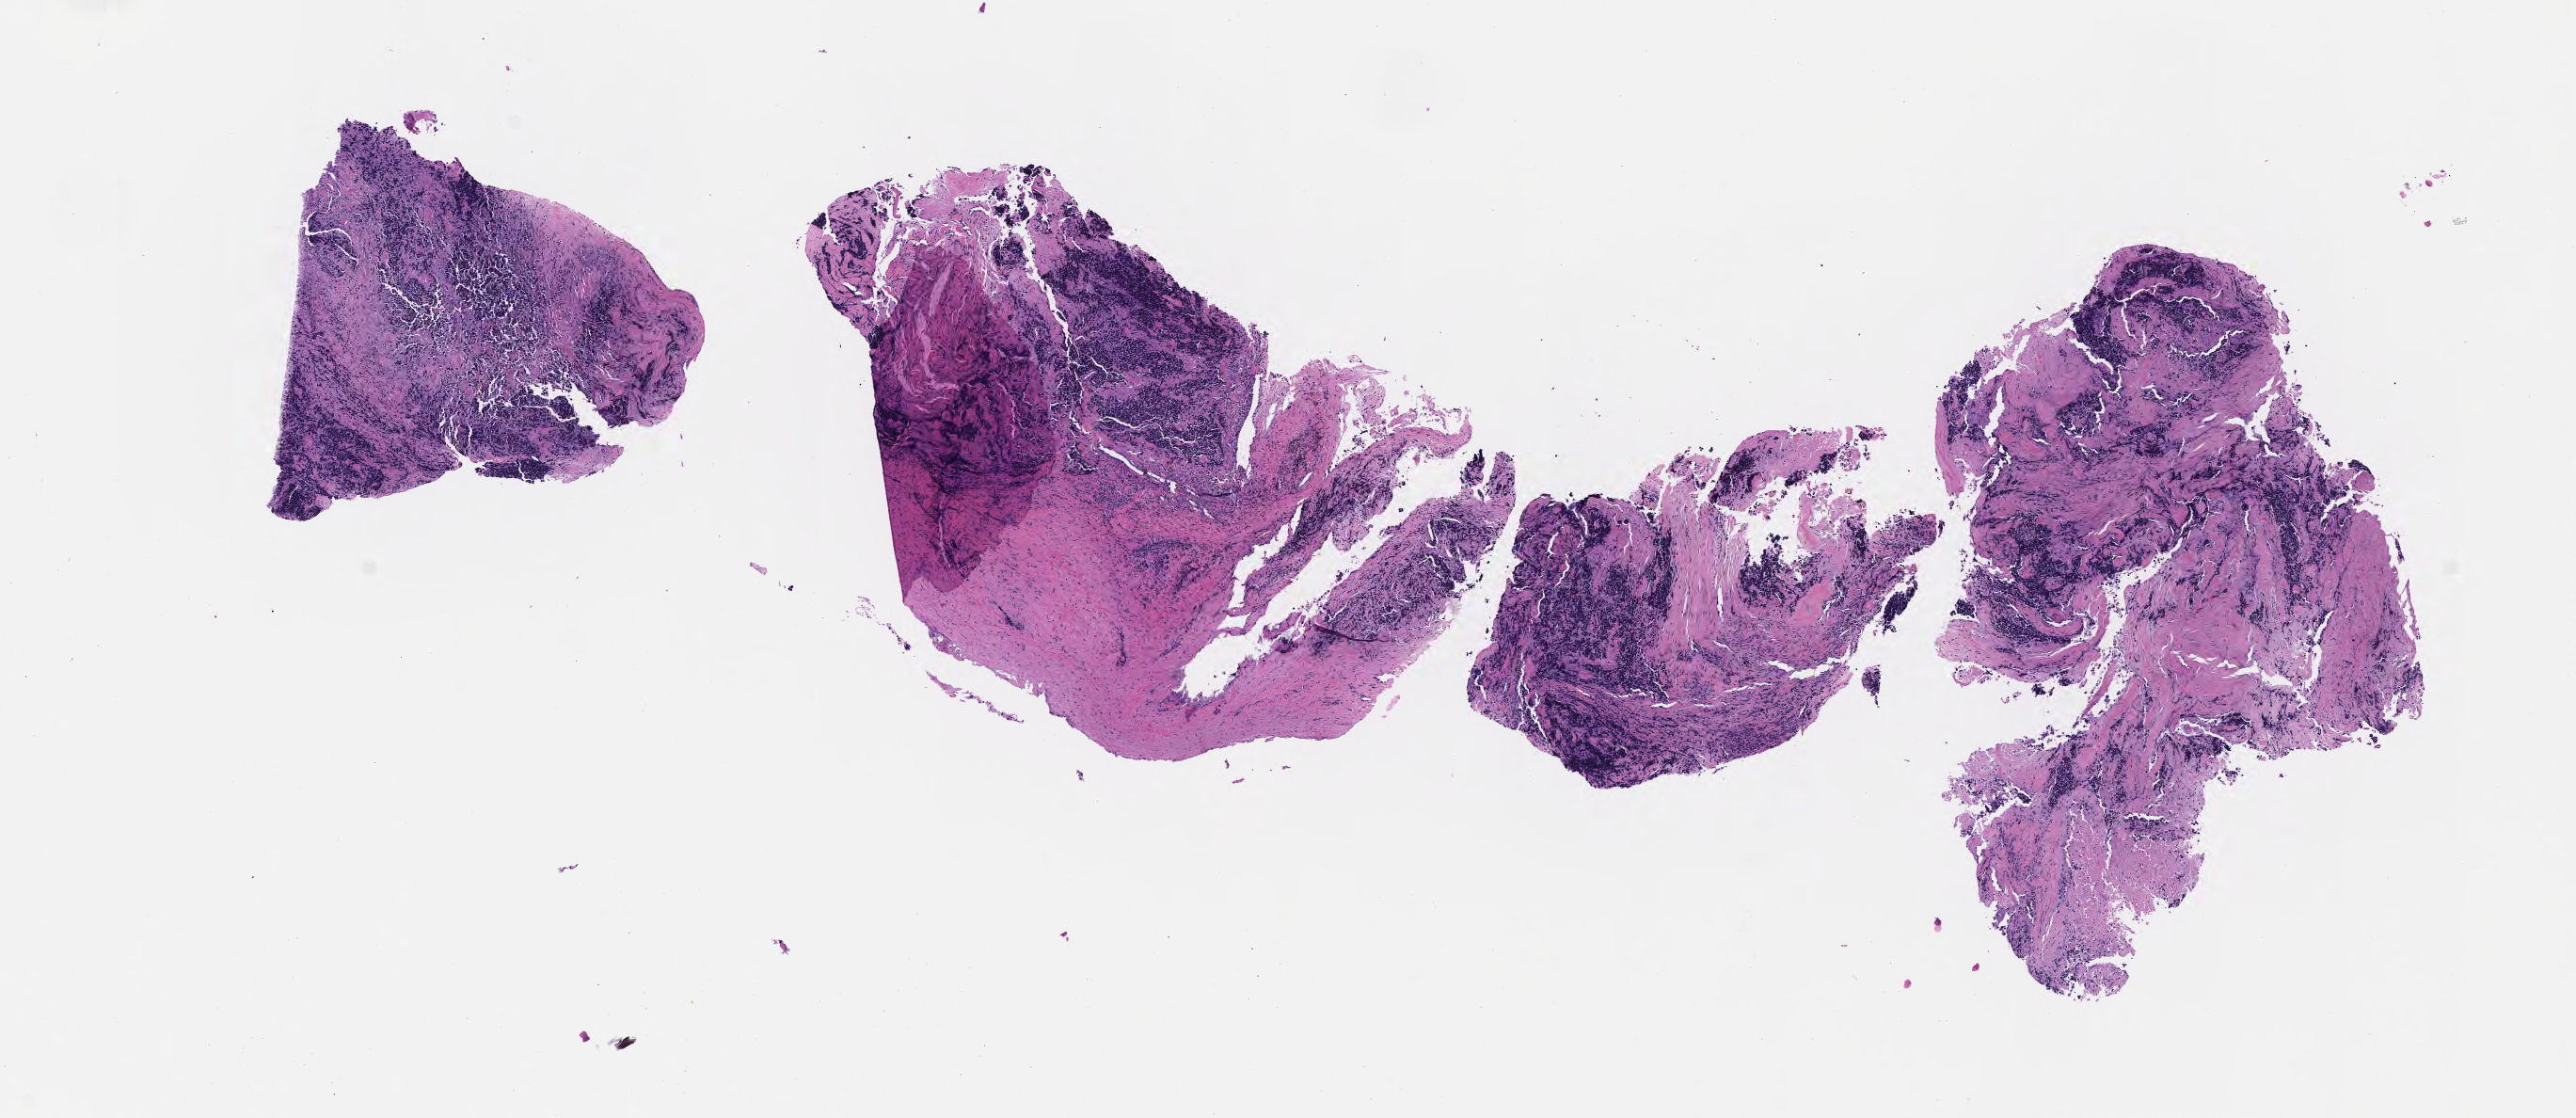
Hematoxylin and eosin (H&E) whole-slide image of tumor tissue from the soft tissue of upper extremity, whole scanned area (about 11.1 x 4.8 mm) shown as a low-resolution overview, formalin-fixed paraffin-embedded section. Patient: female, age 217 months.
Diagnosis (ICD-O-3 morphology term): Alveolar rhabdomyosarcoma.